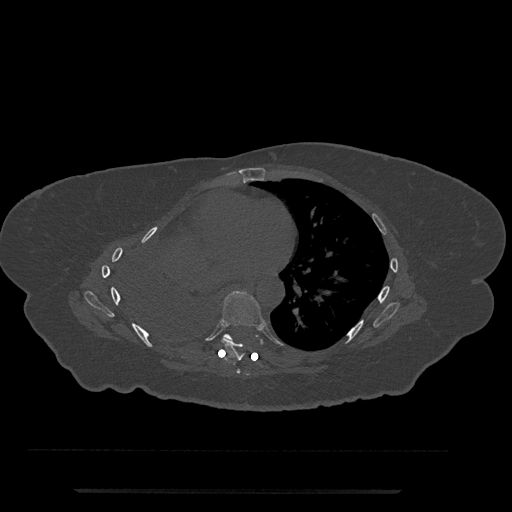
CT including the spine, one axial slice; slice 429 of 797 in the series (ordered by position); bone window (W 1800 / L 400 HU); 512 × 512 image matrix, field of view 440 × 440 mm. Patient: female, 51 years. From the clinical record (not read from this slice): primary cancer: neuro.
Annotated regions visible in this slice (semi-automatically segmented with operator editing):
- T6 vertebra: bounding box (x1, y1, x2, y2) in pixels: (236, 369, 241, 374)
- T7 vertebra: (221, 291, 263, 361)
- T8 vertebra: (223, 334, 233, 340)